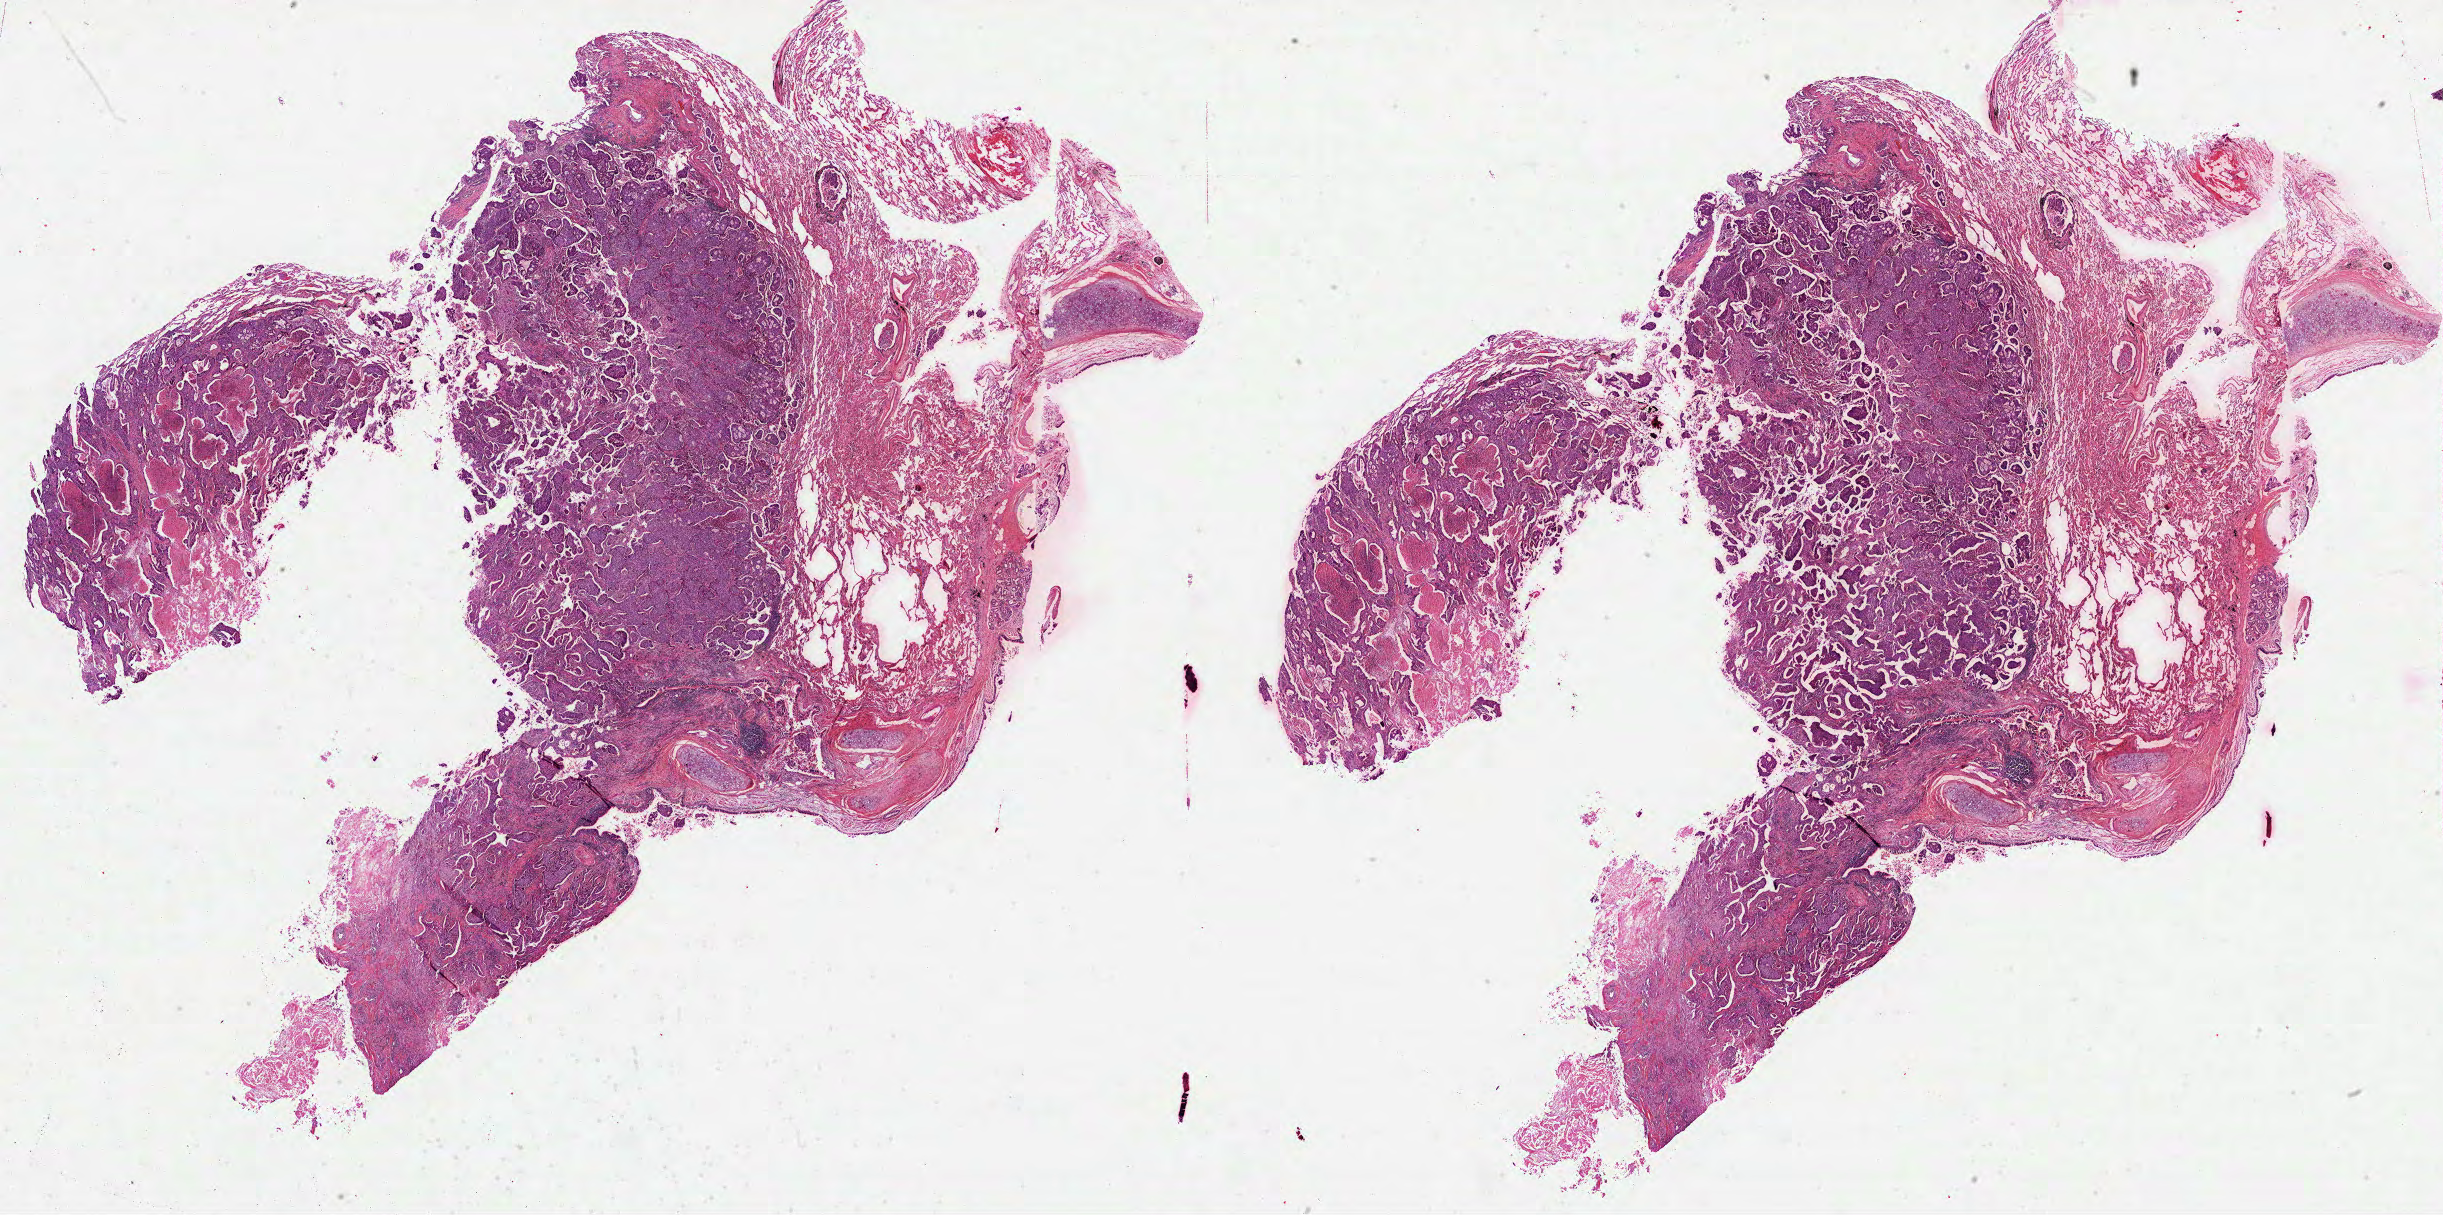
Digitized H&E tissue section (whole slide), low-resolution overview of the scanned area, about 39.4 x 19.6 mm. FFPE section. Sample: primary tumour, lung. Male patient; age at initial diagnosis 77 years.
AJCC pathologic stage: IIIA (4th edition). TNM: T3 N2 M0. Laterality: left. Pathologic diagnosis: Adenocarcinoma, NOS.